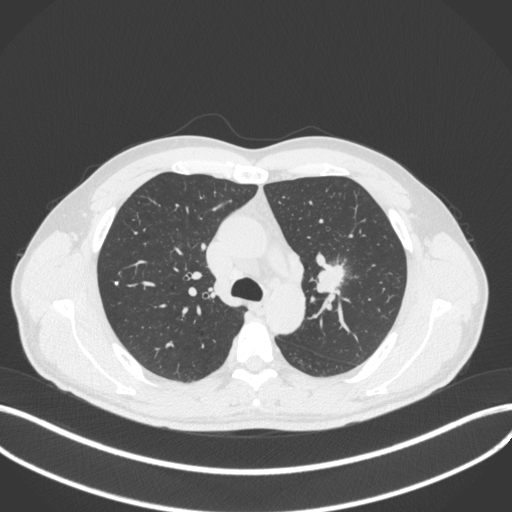
Chest CT, one axial slice. Slice 290 of 383 in the series (ordered by position). Lung window (W 1500 / L -600 HU). 1 mm slice thickness. 512 × 512 image matrix, field of view 400 × 400 mm. Patient: male, 50 years. Case-level facts recorded for this patient, not image findings: clinical TNM (as recorded): T1c N1 M1b.
Annotated regions visible in this slice (rectangle marked by the reading radiologist):
- lung tumour (recorded histology: squamous cell carcinoma): bounding box [x1, y1, x2, y2] px = [309, 254, 348, 295]